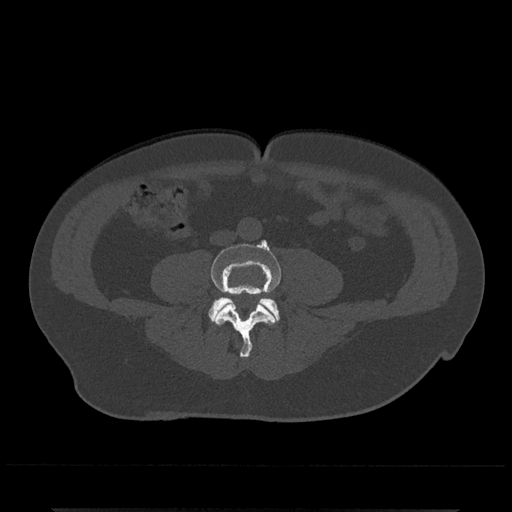
CT including the spine, one axial slice. Position 133 of 797 along the scan axis. 120 kVp. Bone window (W 1800 / L 400 HU). 0.5 mm slice thickness. 512 × 512 image matrix, field of view 393 × 393 mm. Male patient, age 67 years. Case-level facts recorded for this patient, not image findings: primary cancer: prostate.
Structures marked on this image (semi-automatically segmented with operator editing):
- L4 vertebra: bounding box <211,240,281,358> (left, top, right, bottom; pixels)
- L5 vertebra: <208,297,280,321>